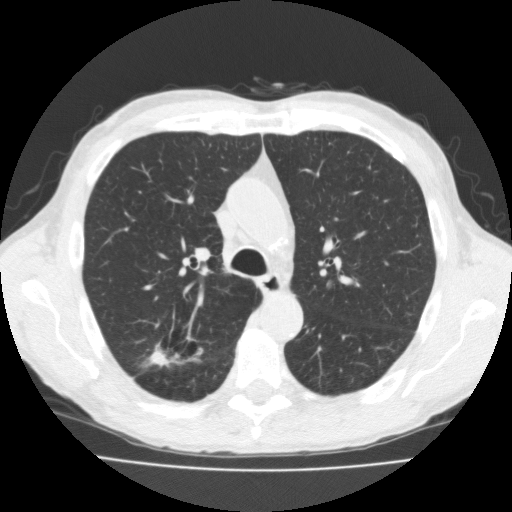
Low-dose screening chest CT, one axial slice. Slice 121 of 181 in the series (ordered by position). Reconstruction kernel FC10. 120 kVp. Lung window (W 1500 / L -600 HU). 512 × 512 image matrix, field of view 350 × 350 mm.
Annotated regions visible in this slice (outlined manually by an expert reader):
- lesion 1 (tumor, upper lobe of right lung): bounding box (x1, y1, x2, y2) in pixels: (150, 348, 174, 366)